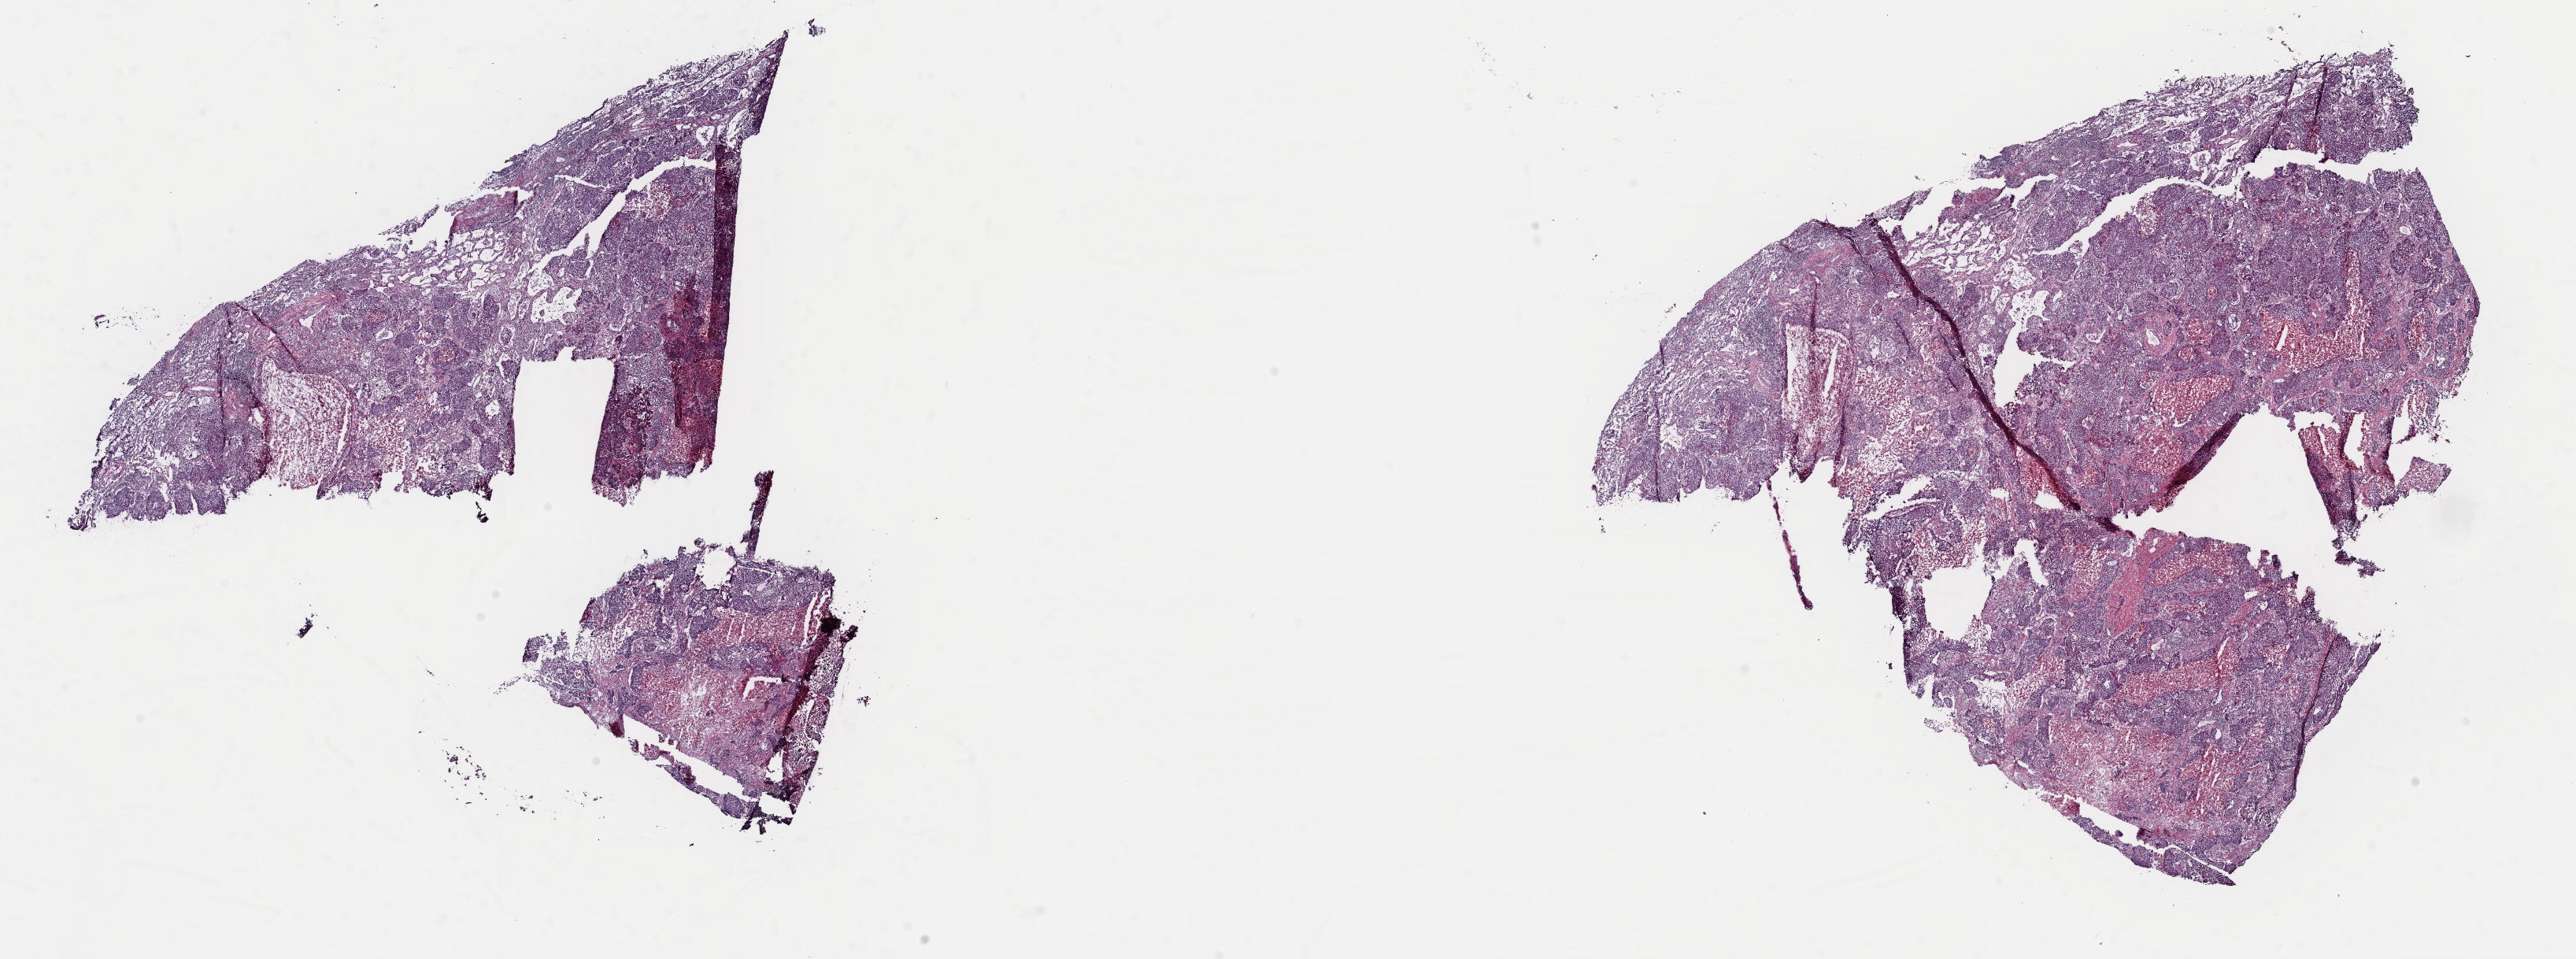
H&E whole-slide image — whole scanned area (about 25.8 x 9.6 mm, acquisition: 40x scan) shown as a low-resolution overview. Frozen section from the top of the tissue portion. Primary tumour sample from the lung. Male, age 61 years at initial diagnosis. Pathologist review of this section (percent, as recorded): tumour cells 70%, tumour nuclei 70%, normal cells 0%, stromal cells 19%, necrosis 11%. Infiltration values recorded for this section: lymphocyte infiltration 4%, monocyte infiltration 2%, neutrophil infiltration 3%.
Histologic diagnosis: Squamous cell carcinoma, NOS (main bronchus). AJCC pathologic stage: IIA. TNM: T2a N1 MX.